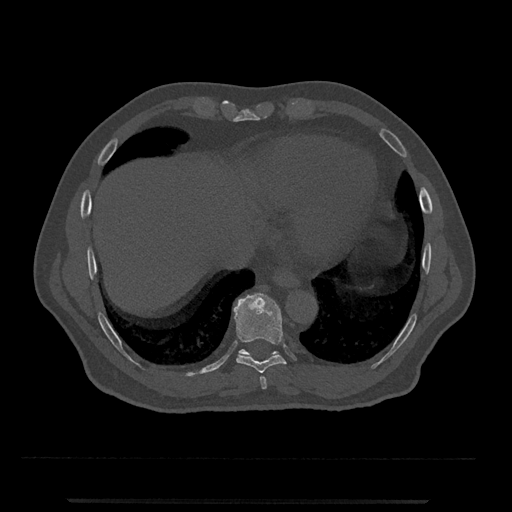
CT including the spine, one axial slice. Position 563 of 797 along the scan axis. Reconstruction kernel Br40s/3. Bone window (W 1800 / L 400 HU). 512 × 512 image matrix. Patient: male, 63 years. From the clinical record (not read from this slice): primary cancer: prostate.
Structures marked on this image (semi-automatically segmented with operator editing):
- T10 vertebra: bounding box <239,349,279,357> (left, top, right, bottom; pixels)
- T8 vertebra: <260,376,267,390>
- T9 vertebra: <233,293,286,373>